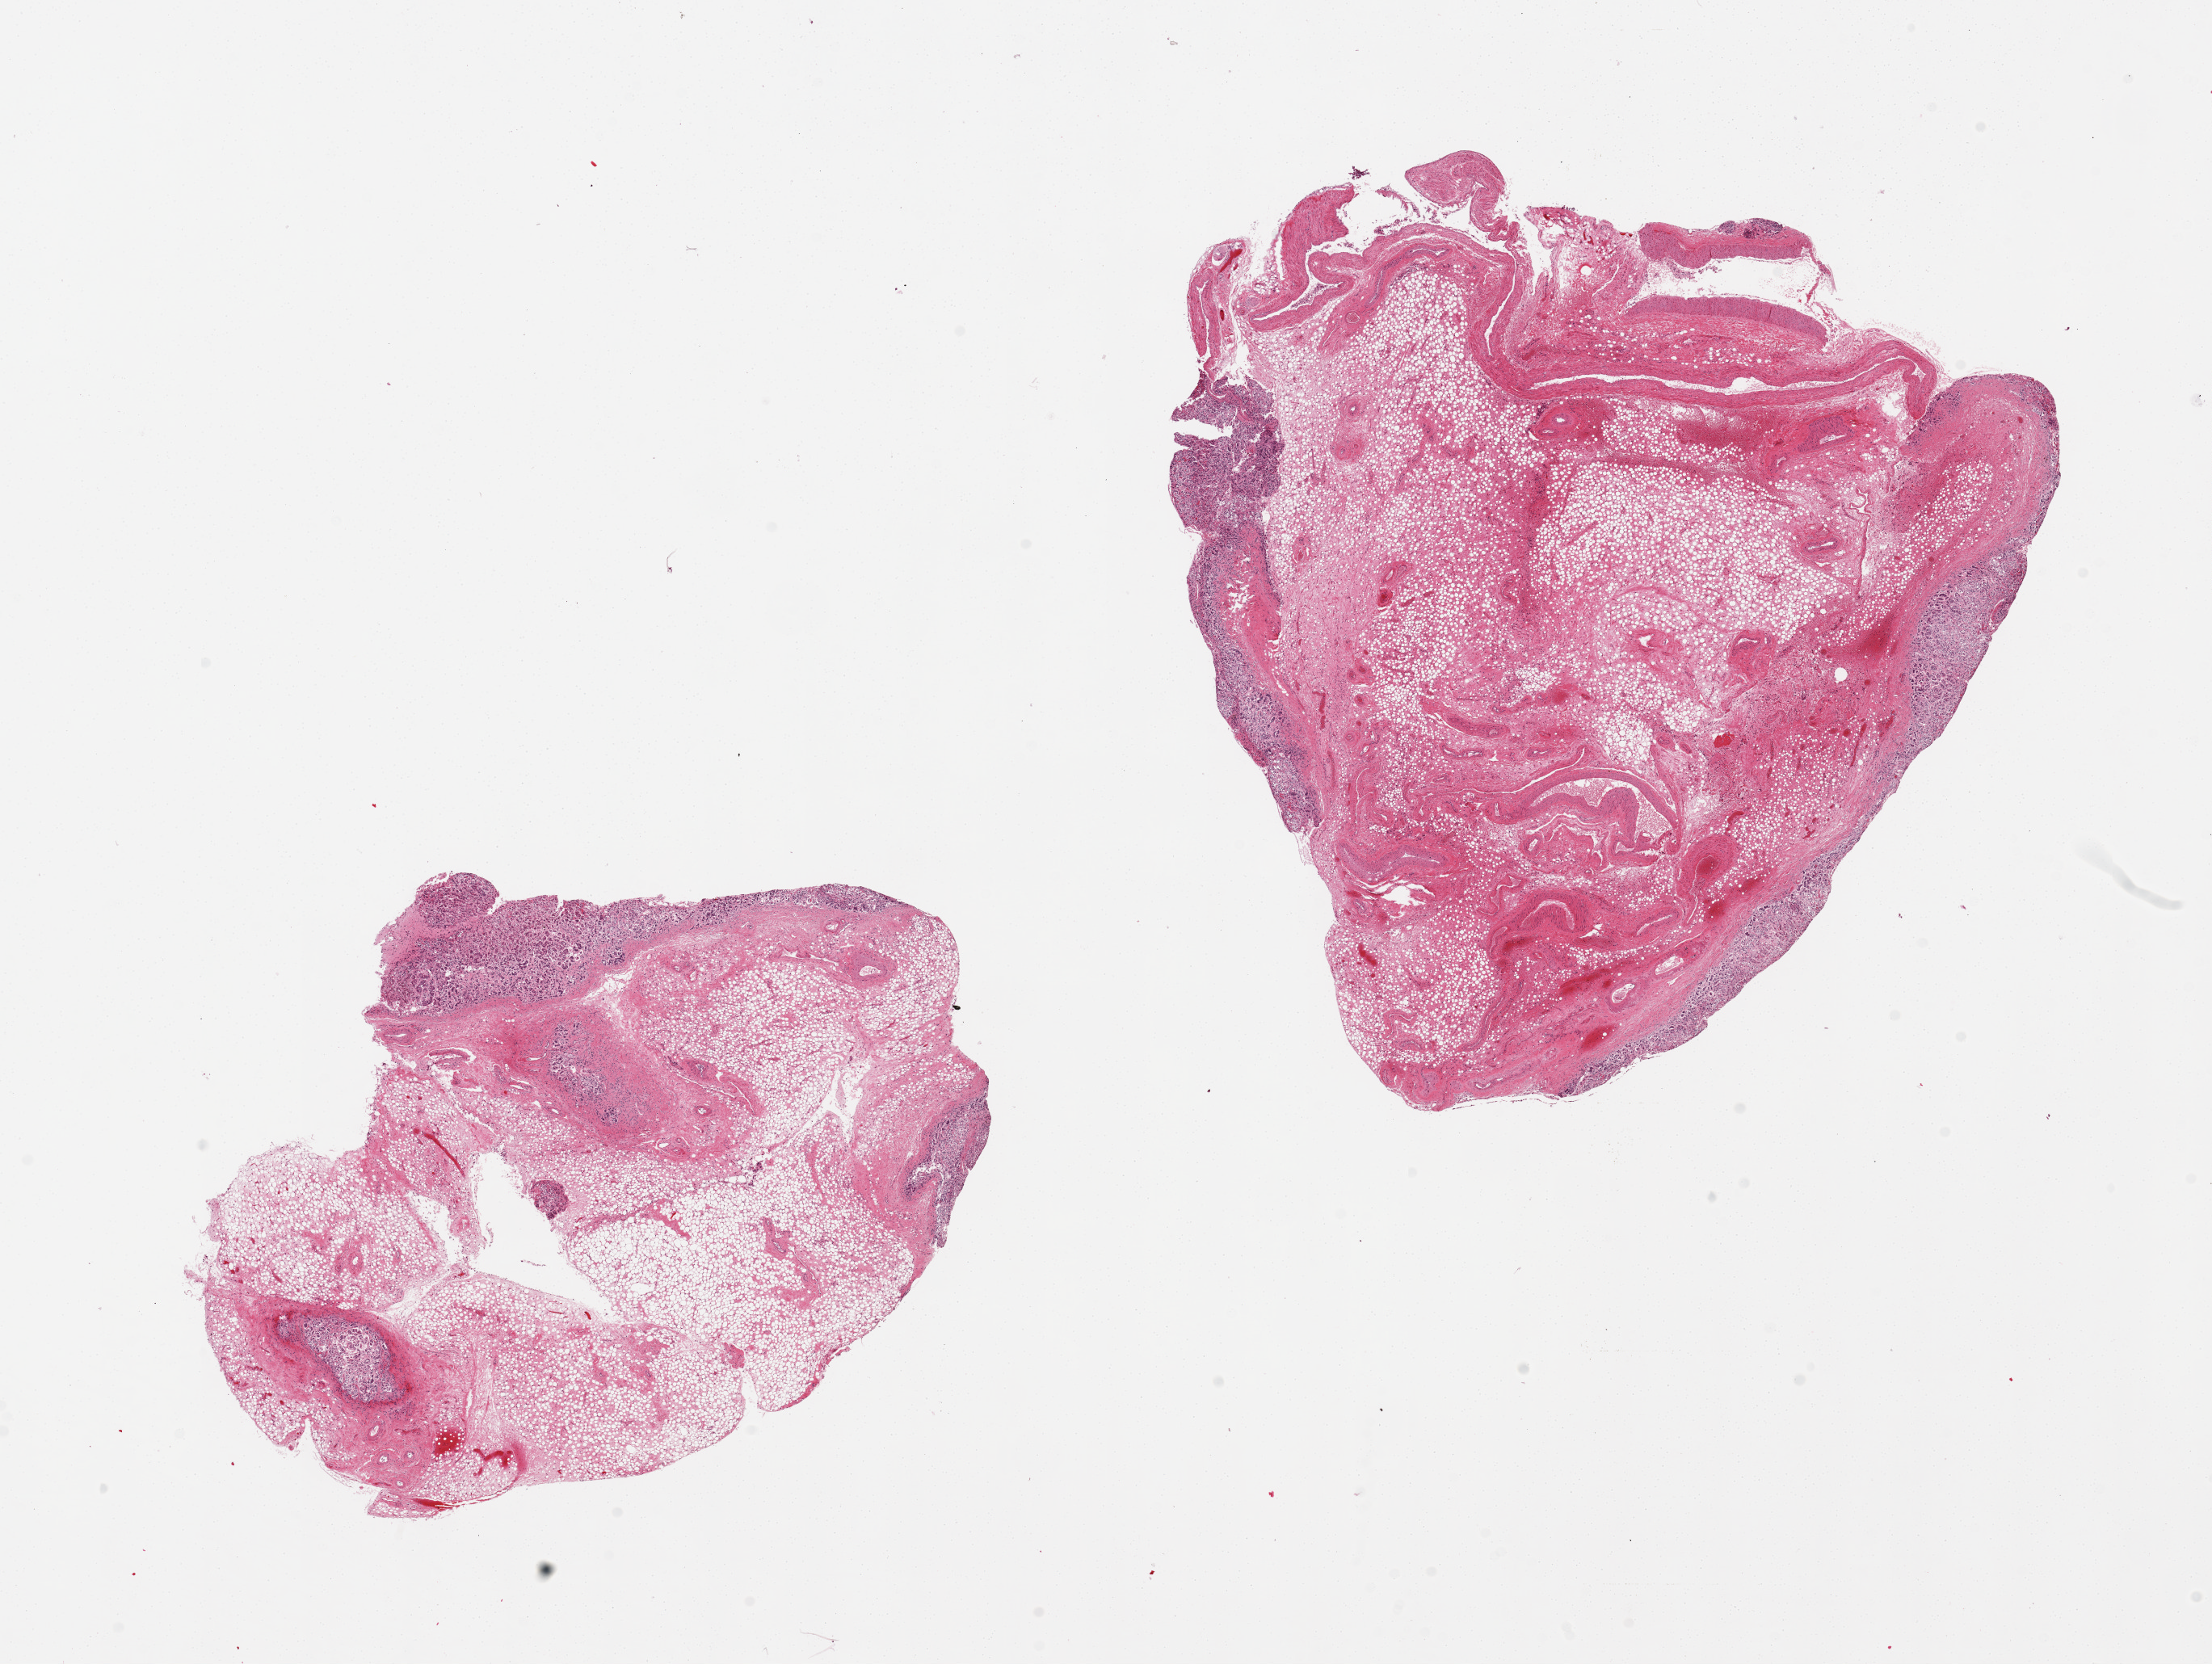
Whole-slide image, hematoxylin and eosin (H&E) stain, brightfield, a low-resolution overview of the entire scanned area, about 21.7 x 16.3 mm (slide scanned at 20x); PAXgene-fixed, paraffin-embedded tissue; target tissue: adrenal gland; donor tissue sample. Donor sex: male.
- reviewer comment on this tissue sample: 2 pieces; predominantly fat with large vessels, ~5-10% autolyzed adrenal